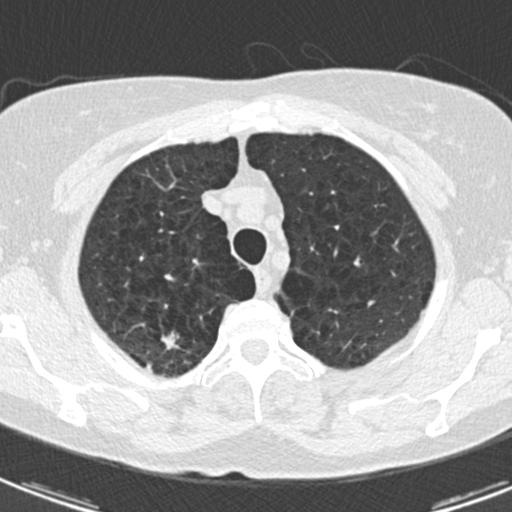
Chest CT (low-dose screening protocol), one axial image, third screening round (two years after baseline), lung window (W 1500 / L -600 HU), slice 27 of 174 in the series. Female participant, aged 59 years at enrolment.
Lesion marked by an expert reader, bounding box <134,320,195,367> (left, top, right, bottom; pixels). Screening reader's record for this exam (one nodule recorded; not confirmed to be the boxed lesion): non-calcified nodule or mass ≥4 mm, right upper lobe, 12 × 7 mm, spiculated (stellate) margins, soft tissue attenuation, pre-existing on the prior screen: yes; interval growth: yes. Official screen result: positive, other.